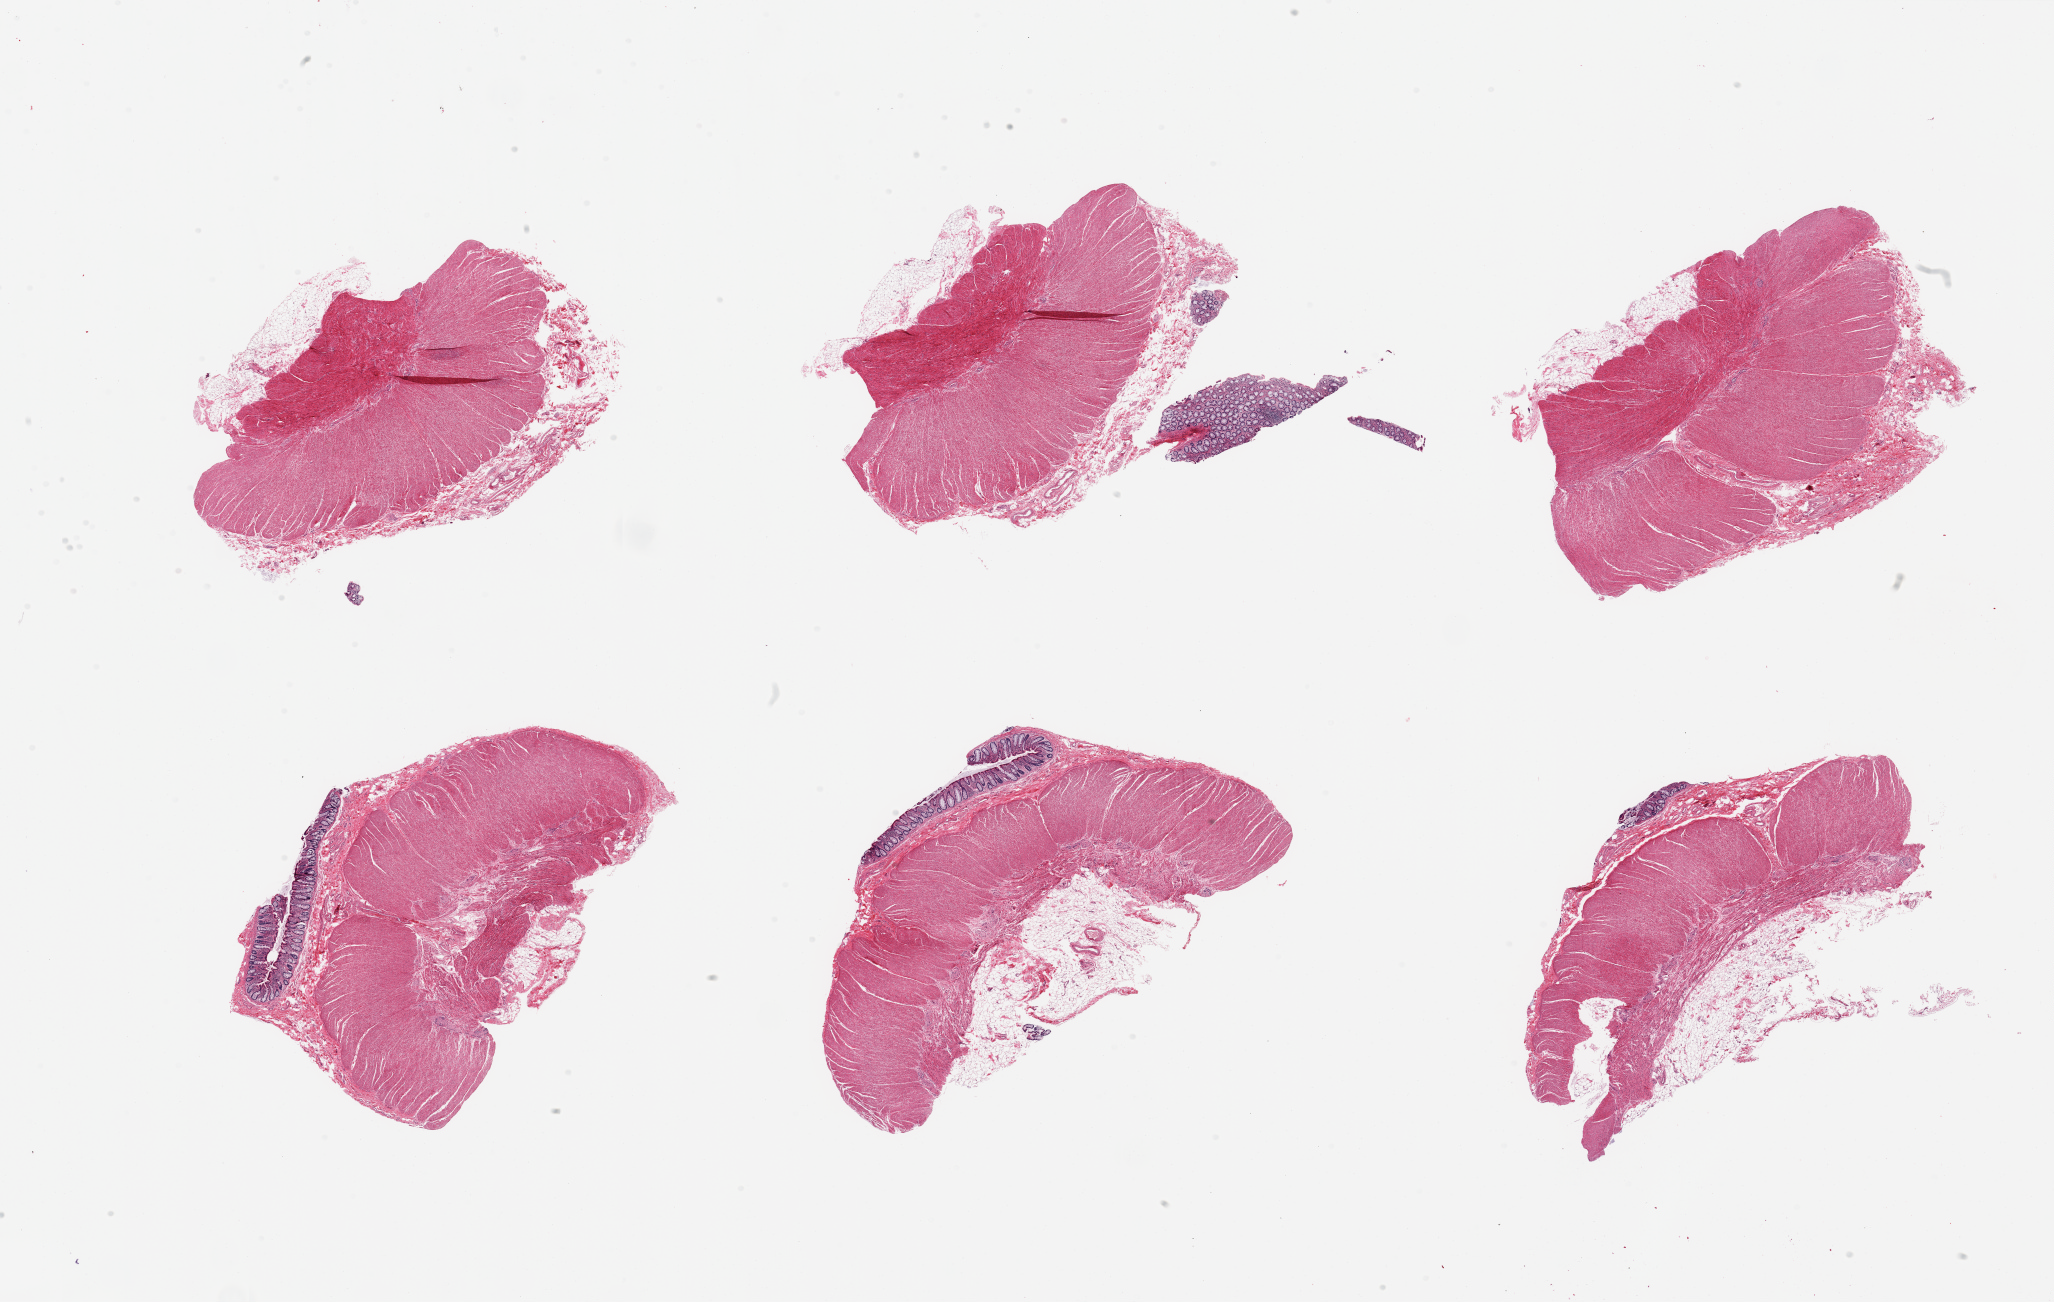
Haematoxylin and eosin whole-slide image, brightfield — low-resolution overview of the scanned area, about 32.5 x 20.6 mm. PAXgene-fixed paraffin-embedded (PFPE) section. Sampled site (target tissue): sigmoid colon. Donor tissue sample. Donor sex: male.
Reviewer comment on this tissue sample: 6 pieces, confirmed target muscularis, ~5-10% 'contaminant mucosa.